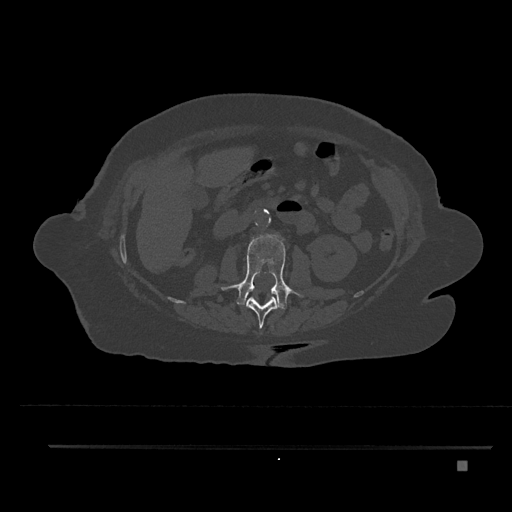
CT including the spine, one axial slice; position 188 of 797 along the scan axis; reconstruction kernel Br40s/3; 120 kVp; bone window (W 1800 / L 400 HU); 0.5 mm slice thickness; 512 × 512 image matrix, field of view 437 × 437 mm. Patient: female, 76 years. From the clinical record (not read from this slice): primary cancer: lung.
Outlined on this slice (semi-automatically segmented with operator editing):
- L1 vertebra: bounding box (x1, y1, x2, y2) in pixels: (246, 295, 278, 329)
- L2 vertebra: (222, 235, 302, 310)